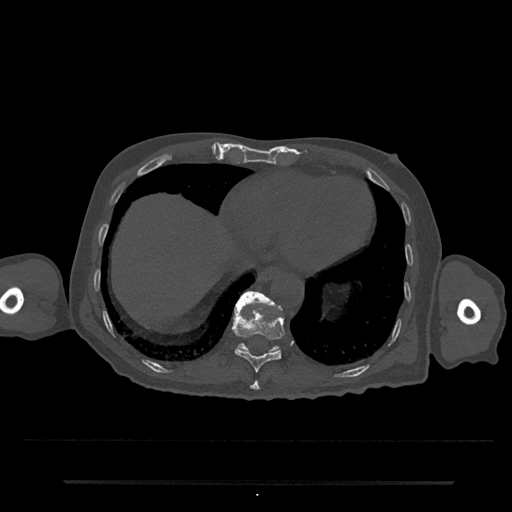
CT including the spine, one axial slice; position 300 of 797 along the scan axis; reconstruction kernel Br40s/3; bone window (W 1800 / L 400 HU); 0.5 mm slice thickness; 512 × 512 image matrix. Male patient, age 74 years. Case-level facts recorded for this patient, not image findings: primary cancer: prostate.
Outlined on this slice (semi-automatic segmentation, software-assisted and operator-edited):
- T10 vertebra: box from (x=232, y=306) to (x=285, y=373) px
- T11 vertebra: (x=234, y=291)–(x=283, y=352)
- T9 vertebra: (x=250, y=380)–(x=260, y=391)